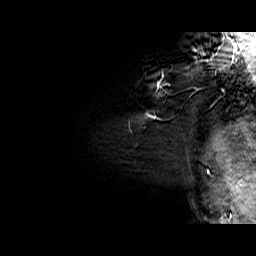
Breast MRI (dynamic contrast-enhanced), one sagittal slice; position 59 of 60 along the scan axis; dynamic contrast-enhanced series, time point 2 of 6 at this slice position (early post-contrast); 1.5 T; TE 6.4 ms, TR 32.9 ms; 4 mm slice thickness; 256 × 256 image matrix, field of view 200 × 200 mm. Female patient. From the clinical record (not read from this slice): setting: breast cancer imaged before/during neoadjuvant chemotherapy; receptor status: HER2-positive.
Outlined on this slice (semi-automatic segmentation, software-assisted and operator-edited):
- analysis volume of interest (the breast-tissue region the enhancement analysis was run in; not a lesion): bounding box <132,62,210,120> (left, top, right, bottom; pixels)
- tumour enhancement mask (voxels above the 100 % enhancement threshold inside the analysis volume of interest): <157,82,160,87>